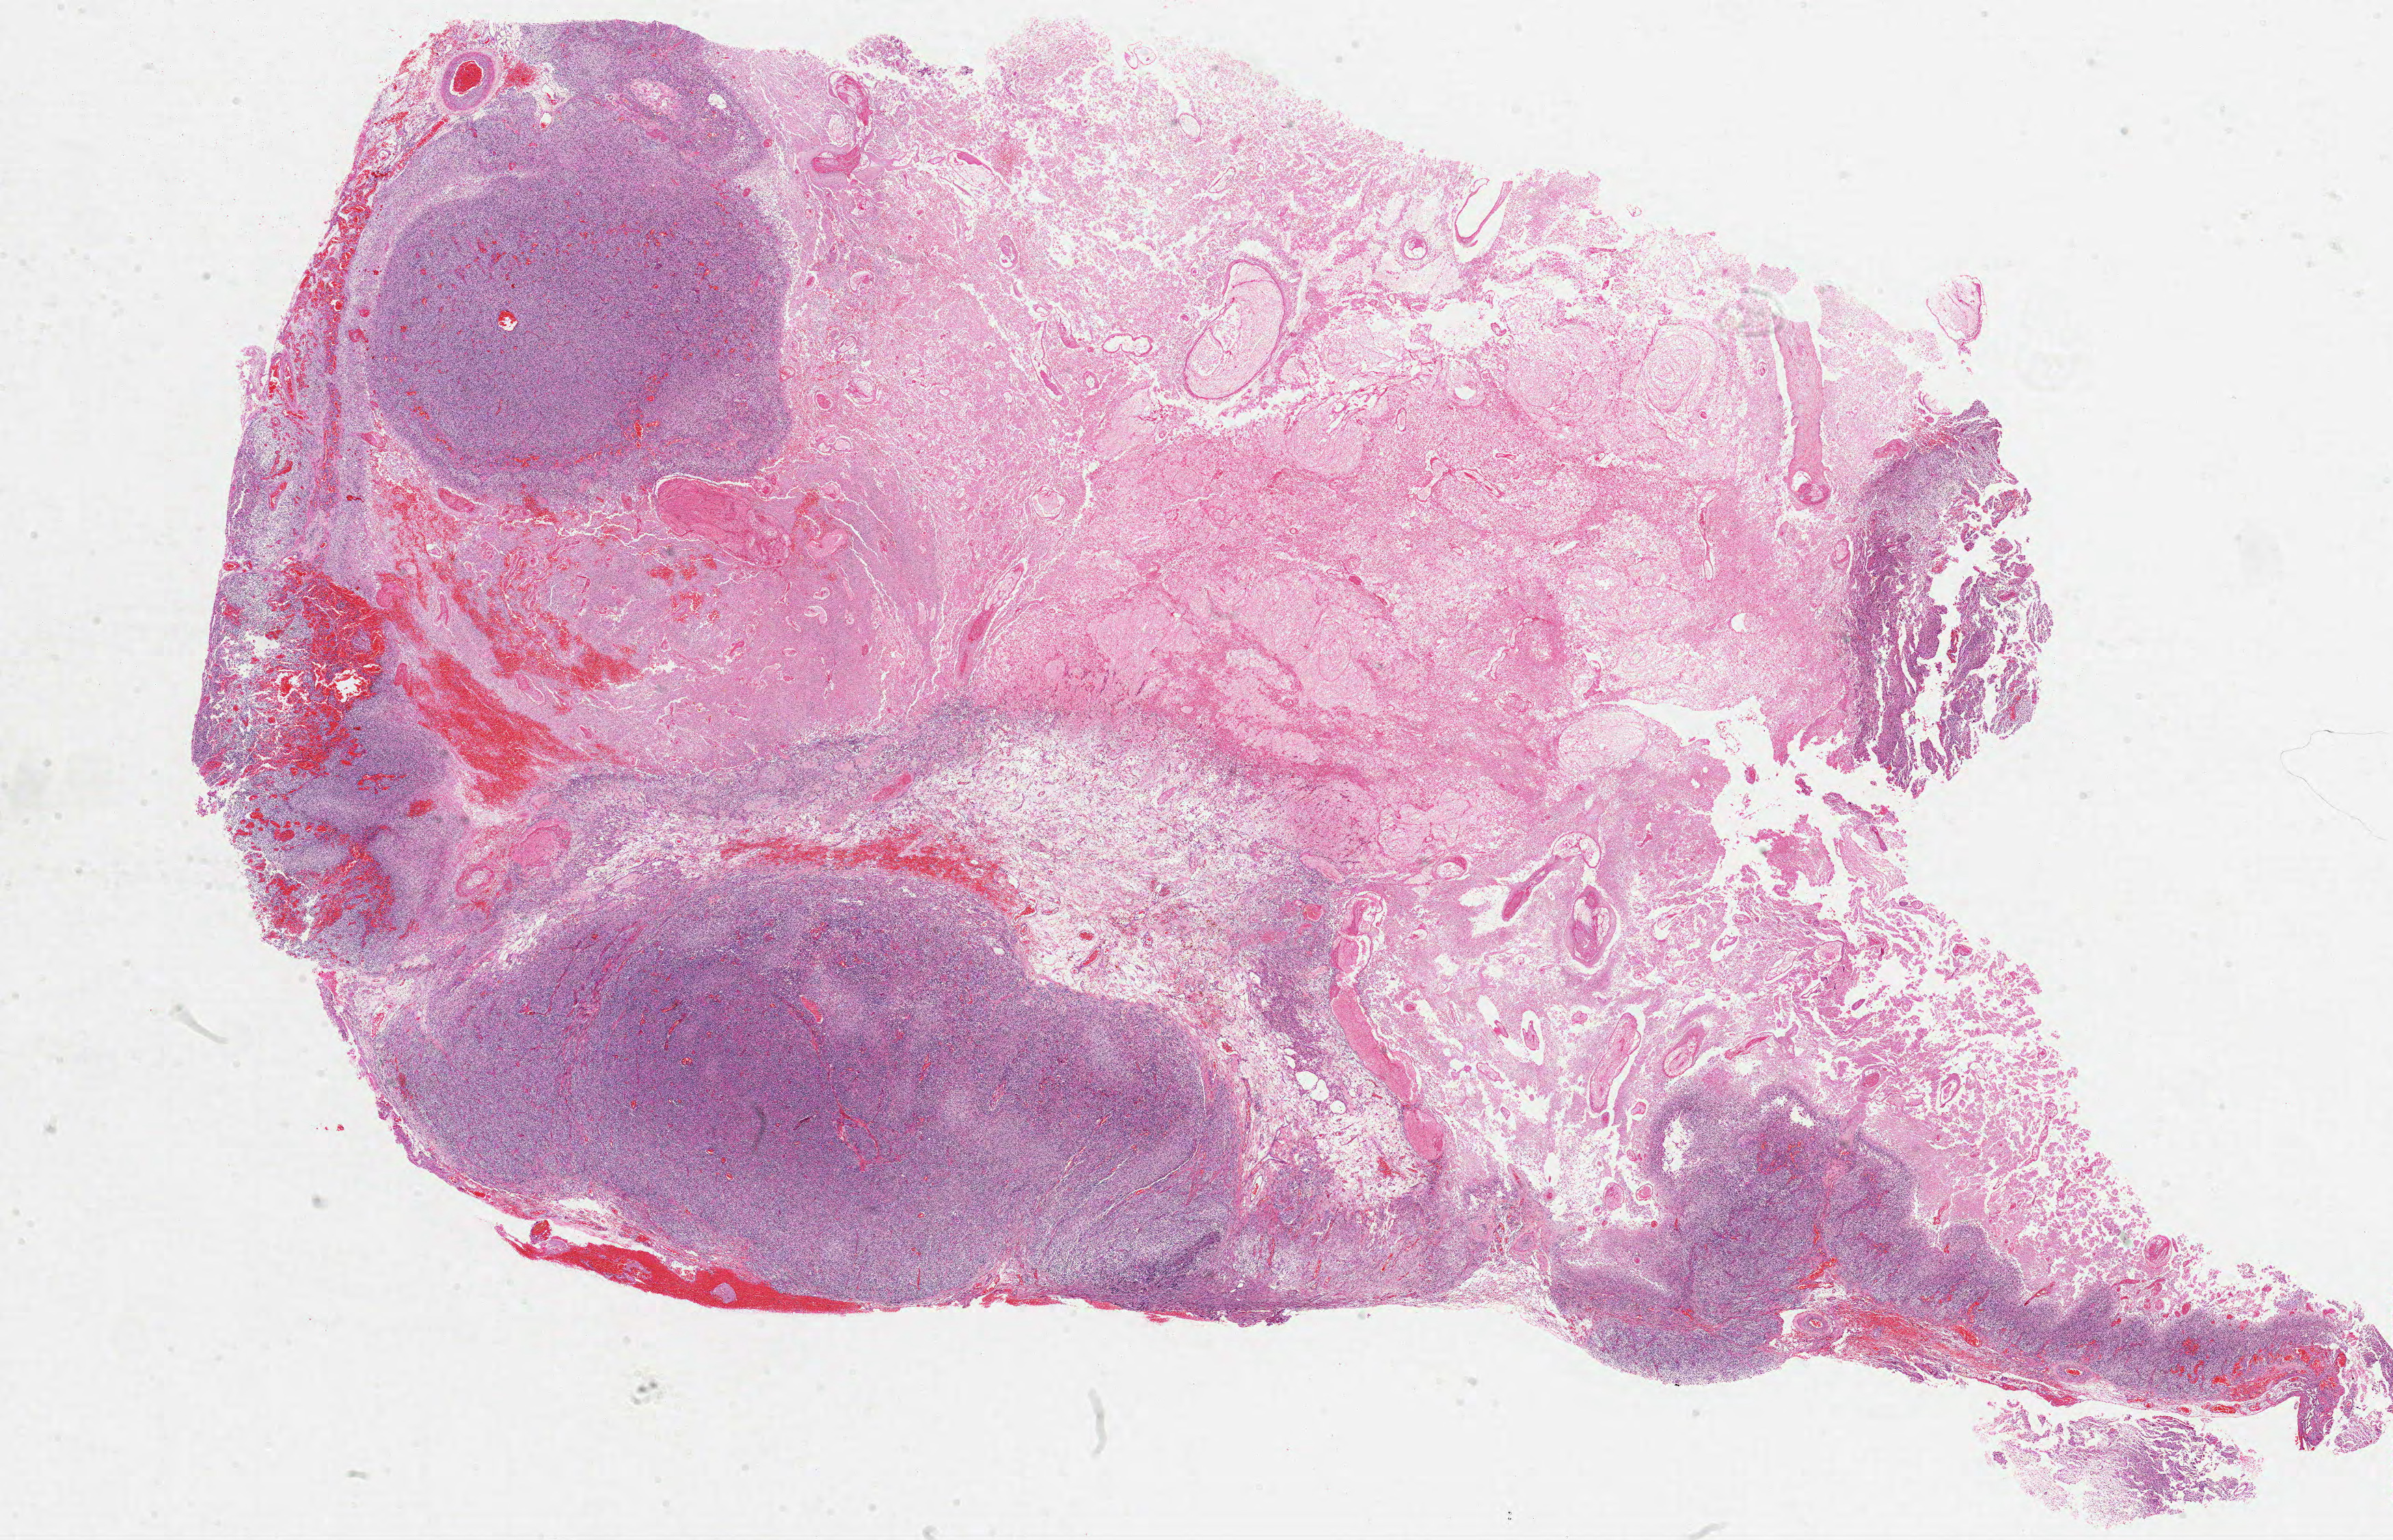
Hematoxylin and eosin (H&E) stained whole-slide image, low-resolution overview of the scanned area, about 28.0 x 18.0 mm (slide scanned at 20x), formalin-fixed paraffin-embedded (FFPE) diagnostic section, brain, primary tumour sample. Patient: male, age at initial diagnosis 74 years.
Diagnosis: Glioblastoma.